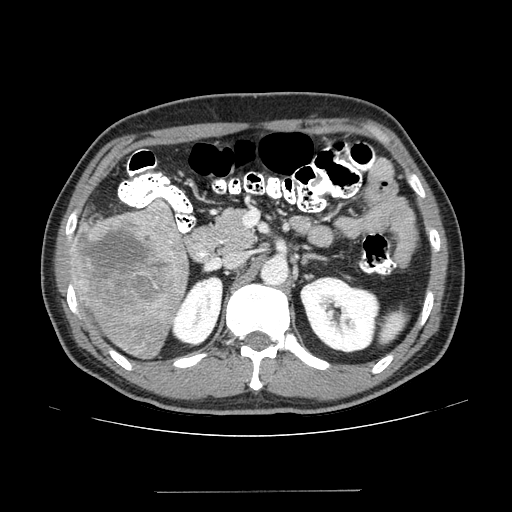
Contrast-enhanced abdominal CT (liver protocol), one axial slice; slice 69 of 131 in the series (ordered by position); reconstruction kernel STANDARD; one of 2 acquisitions stored at this slice position; soft-tissue window (W 400 / L 40 HU); 2.5 mm slice thickness; 512 × 512 image matrix. From the clinical record (not read from this slice): diagnosis: hepatocellular carcinoma (patient treated with transarterial chemoembolisation; whether this scan precedes or follows treatment is not stated here); TNM stage (as recorded): Stage-I; Child-Pugh class: A; tumour differentiation: poorly differentiated; tumour nodularity: uninodular.
Annotated regions visible in this slice (semi-automatic segmentation, software-assisted and operator-edited):
- liver parenchyma outside the tumour (the mass and vessels are separate outlines, so this box may not span the whole liver): box from (x=68, y=201) to (x=188, y=358) px
- mass: (x=72, y=204)–(x=186, y=325)